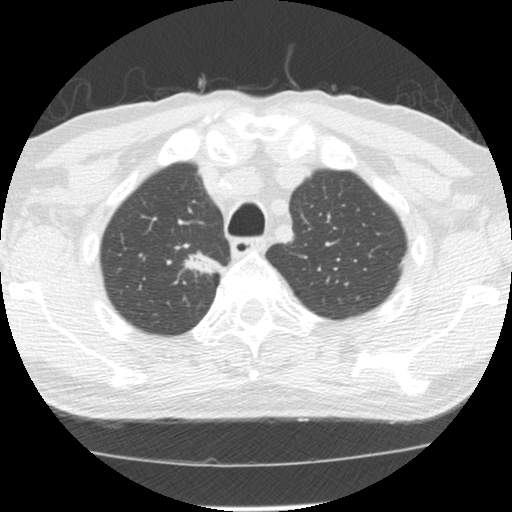
Low-dose screening chest CT, one axial slice. Position 111 of 139 along the scan axis. 120 kVp. Lung window (W 1500 / L -600 HU). 2.5 mm slice thickness. 512 × 512 image matrix.
Annotated regions visible in this slice (outlined manually by an expert reader):
- lesion 1 (tumor, upper lobe of right lung): bounding box <183,251,223,276> (left, top, right, bottom; pixels)